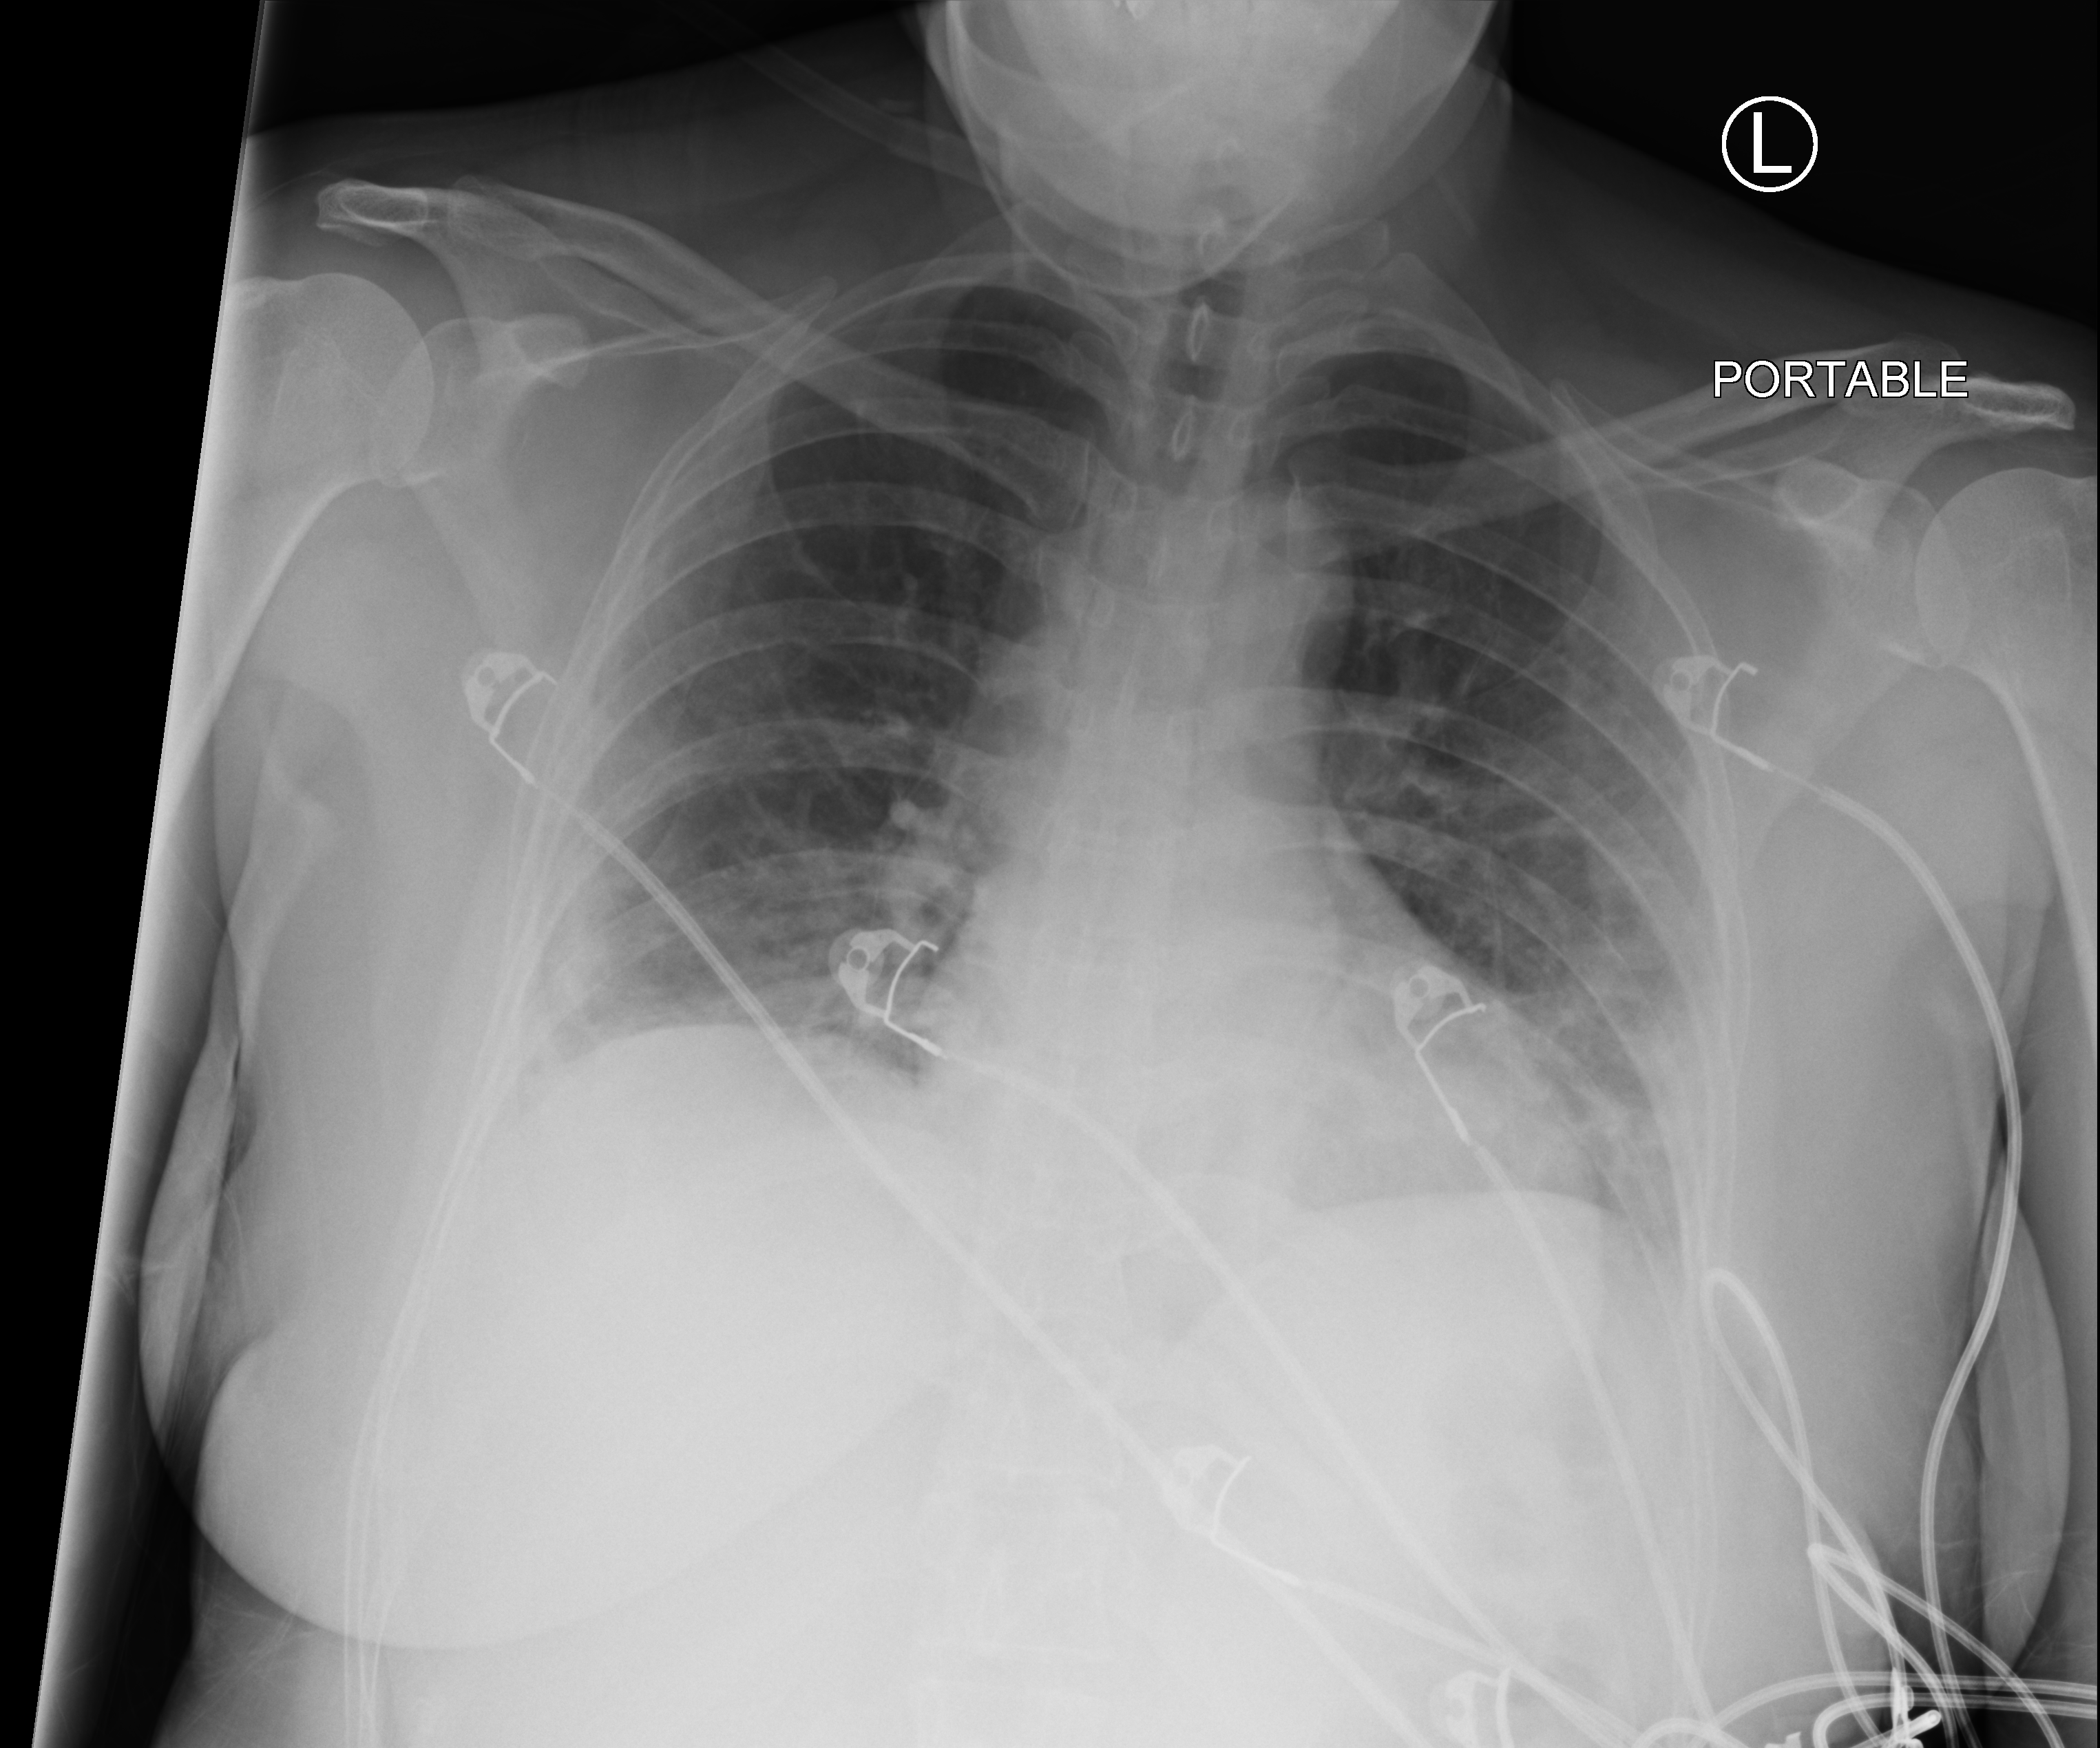
Bedside chest radiograph (computed radiography), anteroposterior (AP) projection. Patient hospitalised with COVID-19; female, aged 18–59 years.
Hospital-stay facts (about this admission, not read from this image; timing relative to this image not recorded): COPD (admission record): no; admitted to intensive care during this hospital stay: no; mechanically ventilated during this hospital stay: no.